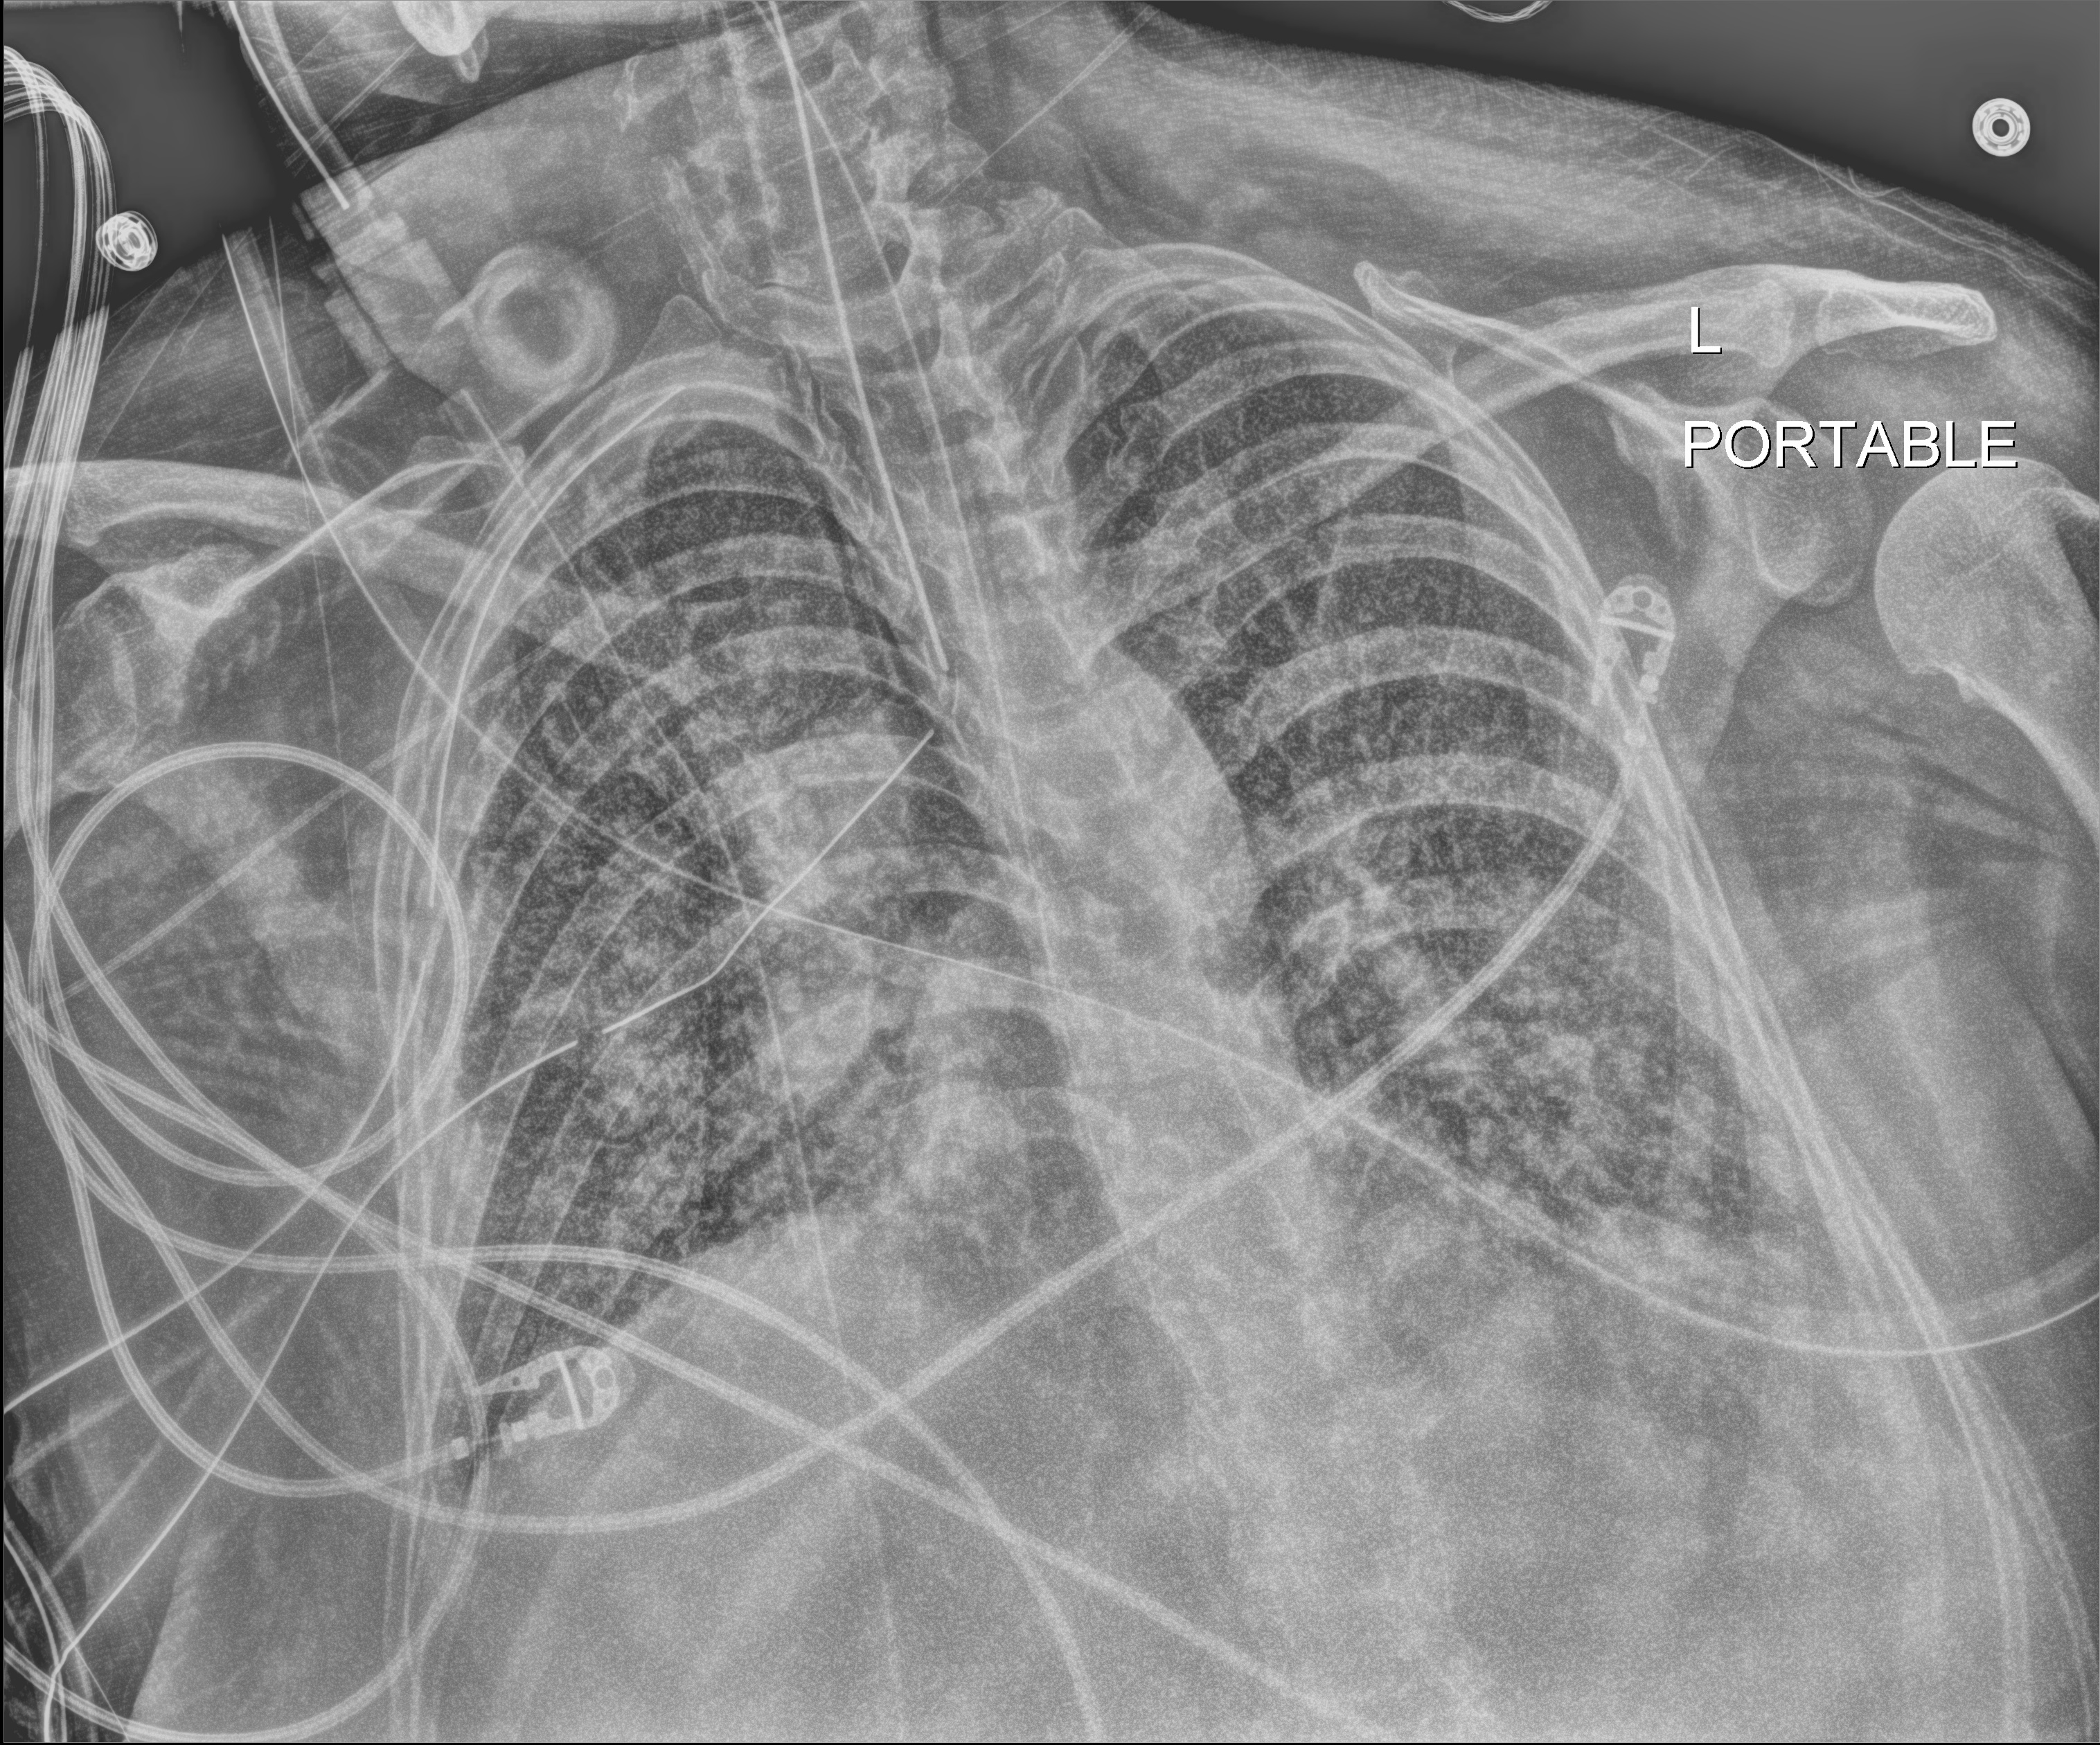
Bedside chest radiograph (digital radiography), anteroposterior (AP) projection. Adult patient hospitalised with COVID-19, age 18–59 years.
Hospital-stay facts (about this admission, not read from this image; timing relative to this image not recorded): admitted to intensive care during this hospital stay: yes; diabetes (admission record): no.